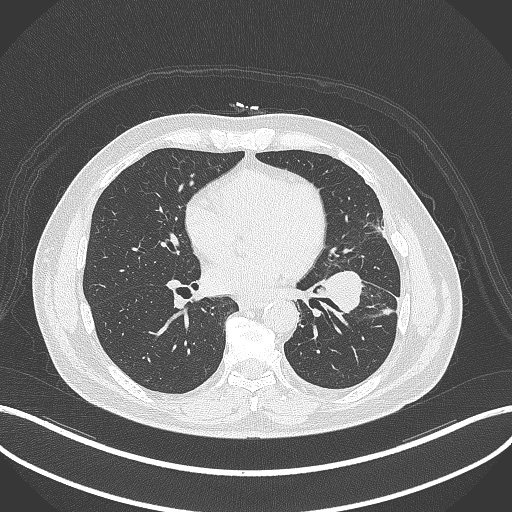
Chest CT, one axial slice. Slice 160 of 230 in the series (ordered by position). 120 kVp. Lung window (W 1500 / L -600 HU). 1 mm slice thickness. 512 × 512 image matrix, field of view 400 × 400 mm. Male patient, age 68 years. Case-level facts recorded for this patient, not image findings: clinical TNM (as recorded): T2b N0 M0.
Annotated regions visible in this slice (bounding box drawn by a radiologist):
- lung tumour (recorded histology: squamous cell carcinoma): bounding box (x1, y1, x2, y2) in pixels: (317, 264, 367, 317)